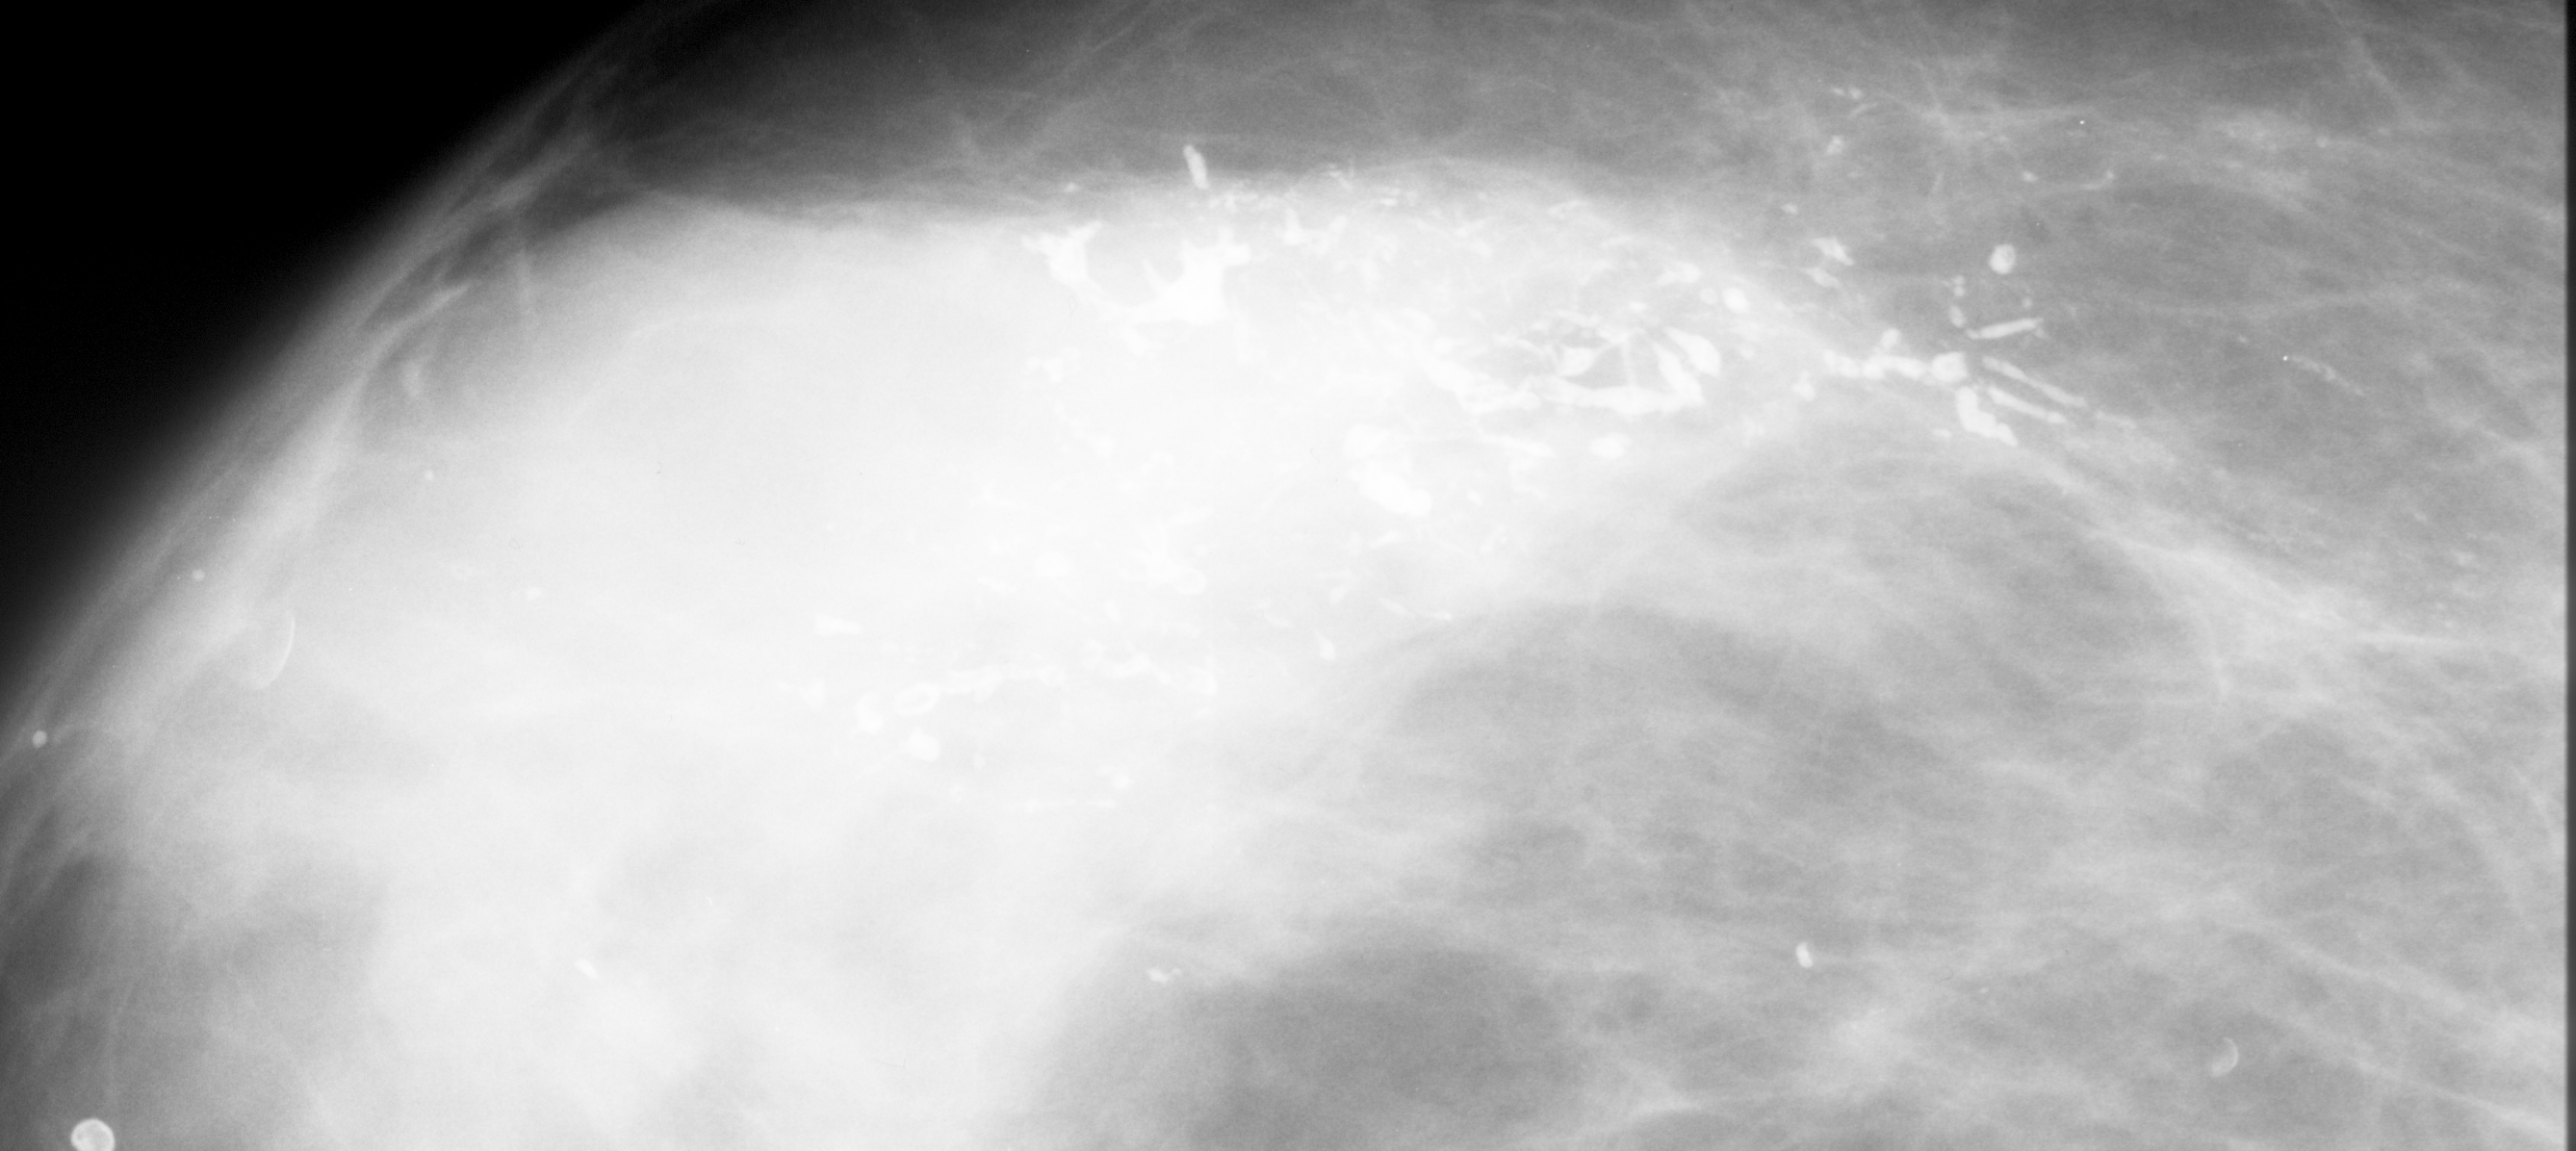
Cropped region of a digitized screen-film mammogram centred on a radiologist-marked abnormality; left breast; CC view.
Marked abnormality: calcifications, morphology pleomorphic, distribution segmental; BI-RADS assessment category 5; subtlety rating 5 on a 1 (subtle) to 5 (obvious) scale; pathology (as recorded): malignant.